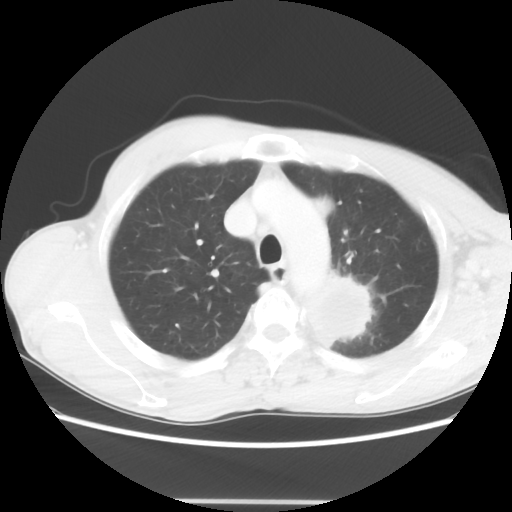
Chest CT, one axial slice. Slice 50 of 62 in the series (ordered by position). Reconstruction kernel STANDARD. 100 kVp. Lung window (W 1500 / L -600 HU). 512 × 512 image matrix, field of view 360 × 360 mm. Male patient, age 61 years. From the clinical record (not read from this slice): clinical TNM (as recorded): T3 N1 M1.
Annotated regions visible in this slice (bounding box drawn by a radiologist):
- lung tumour (recorded histology: adenocarcinoma): box from (x=298, y=272) to (x=380, y=367) px
- lung tumour (recorded histology: adenocarcinoma): (x=312, y=195)–(x=336, y=225)